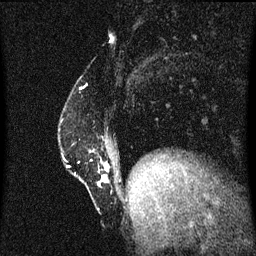
Breast MRI (dynamic contrast-enhanced), one sagittal slice; slice 12 of 60 in the series (ordered by position); dynamic contrast-enhanced series, image 2 of 3 at this slice position (ordered by acquisition); 1.5 T; TE 4.2 ms, TR 8.4 ms; 2 mm slice thickness; 256 × 256 image matrix, field of view 200 × 200 mm. Patient: female, 52 years. From the clinical record (not read from this slice): setting: breast cancer imaged before/during neoadjuvant chemotherapy; receptor status: HER2-positive.
Outlined on this slice (semi-automatic segmentation, software-assisted and operator-edited):
- analysis volume of interest (the breast-tissue region the enhancement analysis was run in; not a lesion): bounding box (x1, y1, x2, y2) in pixels: (63, 152, 112, 185)
- tumour enhancement mask (voxels above the 70 % enhancement threshold inside the analysis volume of interest): (103, 170, 109, 183)